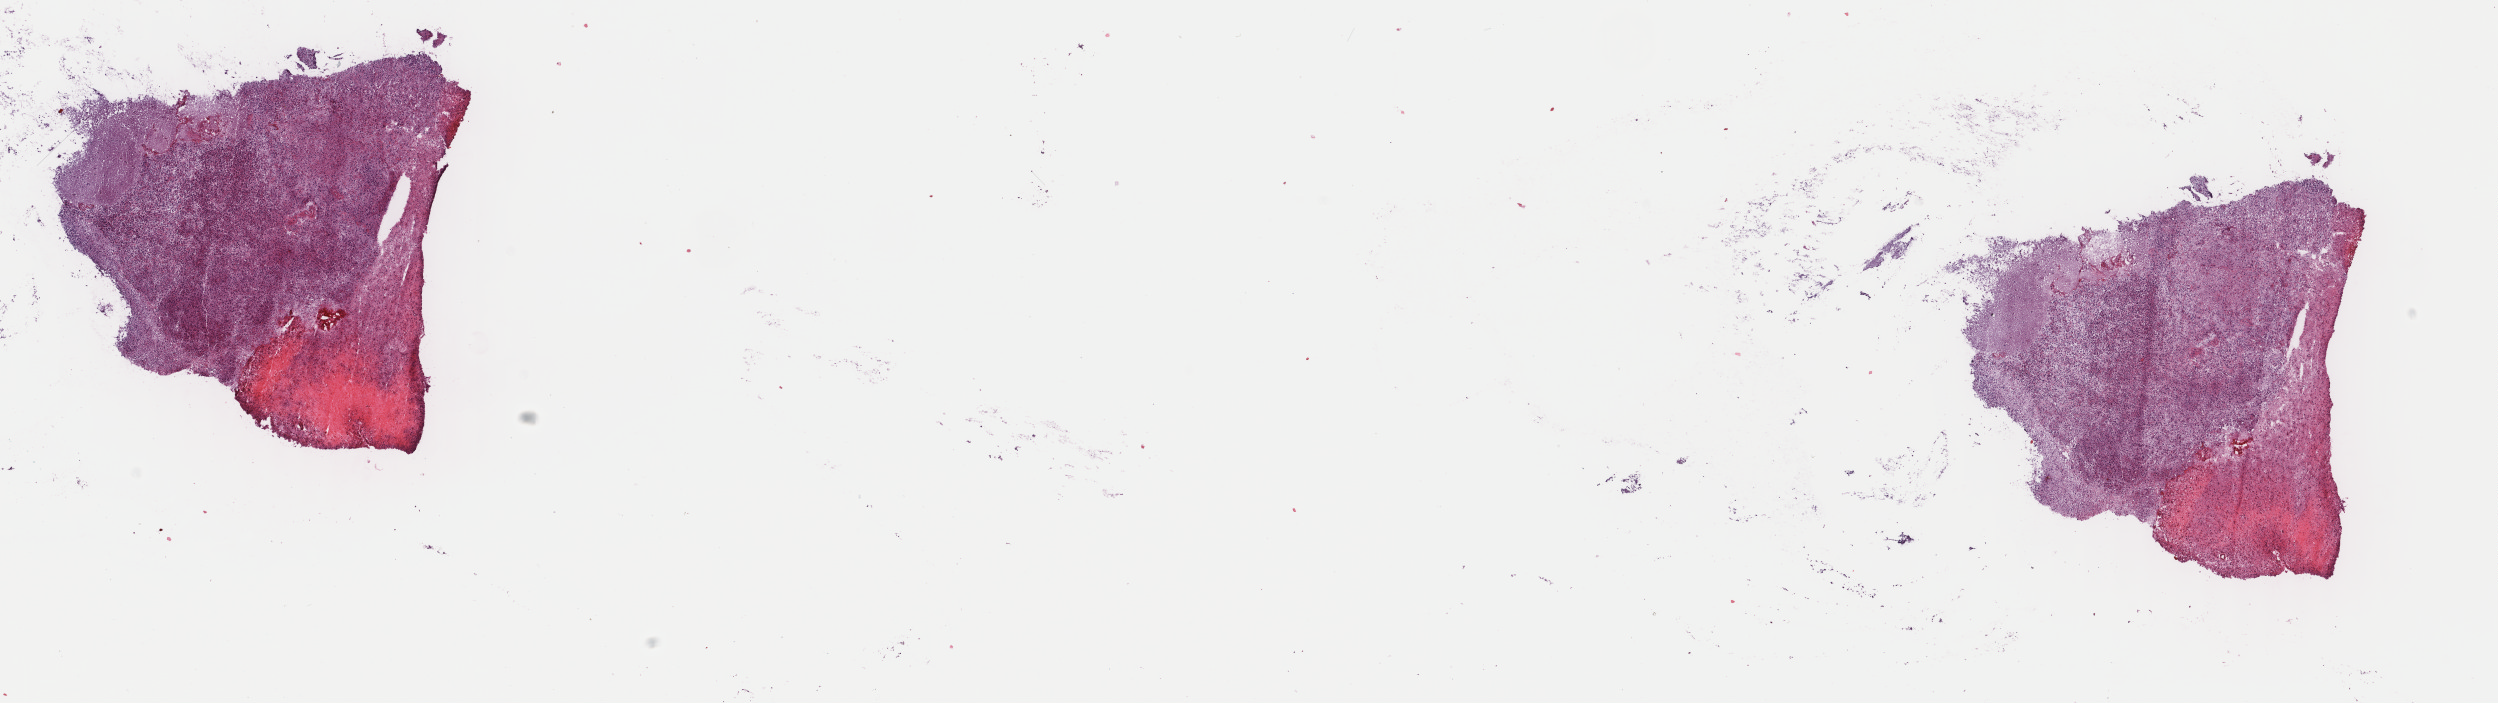
Whole-slide histology image, Hematoxylin and eosin (H&E) stained — a low-resolution overview of the entire scanned area, about 19.8 x 5.6 mm (acquisition: 40x scan). Frozen section from the top of the tissue portion. Brain, primary tumour sample. Male patient; age at initial diagnosis 57 years. Histologic grade: G3 (poorly differentiated). Pathologist review of this section (percent, as recorded): tumour cells 70%, tumour nuclei 90%, normal cells 5%, stromal cells 25%, necrosis 0%. Inflammatory infiltration, as recorded: lymphocyte infiltration 0%, monocyte infiltration 0%, neutrophil infiltration 0%.
Histologic diagnosis: Astrocytoma, anaplastic.